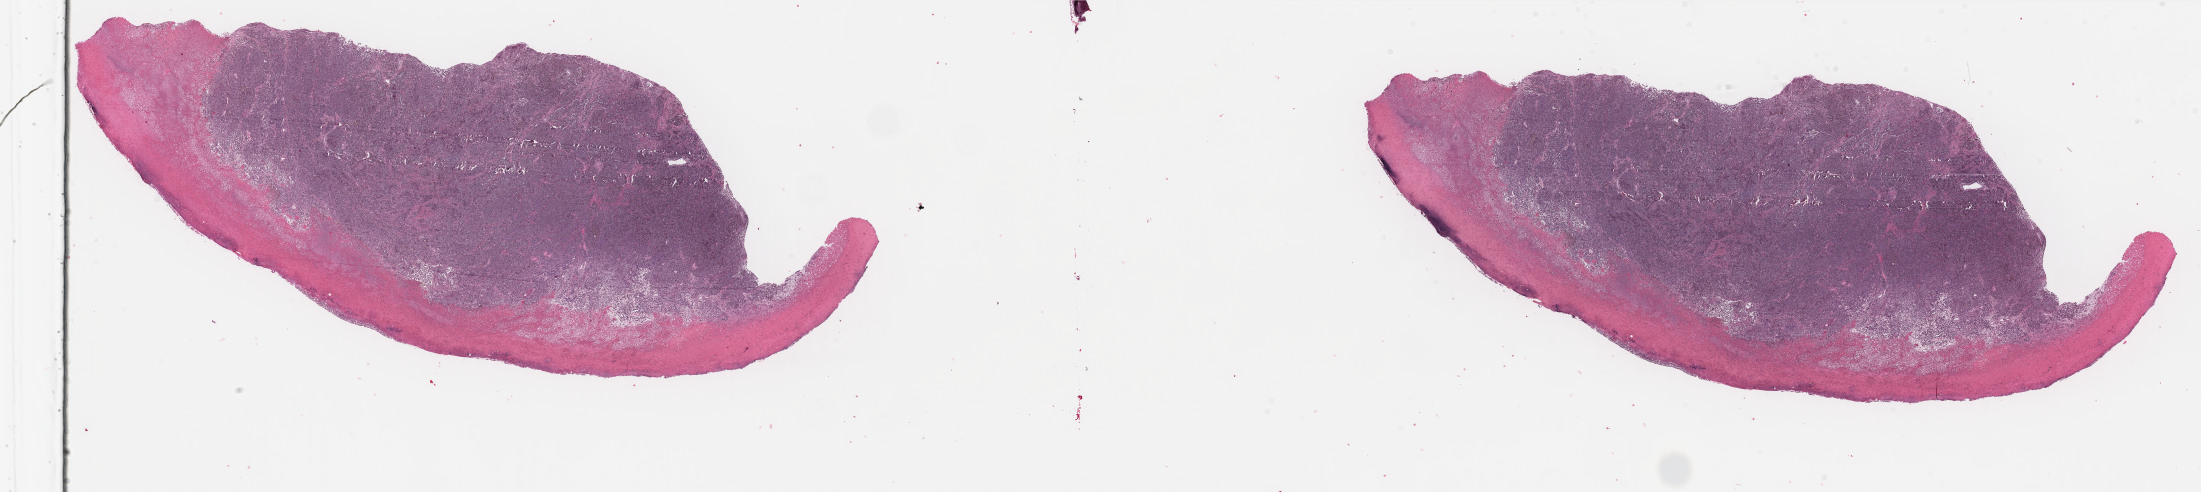
Hematoxylin and eosin (H&E) stained whole-slide image — a low-resolution overview of the entire scanned area, about 34.8 x 7.8 mm (from a 40x scan); FFPE section; primary tumour sample from the skin. Female, age 54 years at initial diagnosis.
• diagnosis: Superficial spreading melanoma